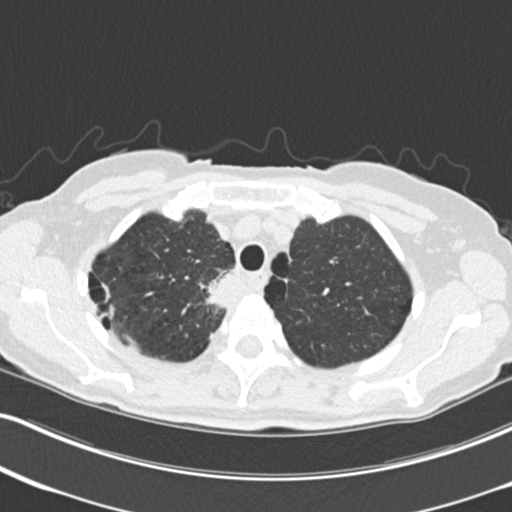
Axial slice from a low-dose chest CT screening exam; third annual screen; lung window (W 1500 / L -600 HU); 120 kVp; slice 45 of 226 in the series; 512 × 512 image matrix. Female participant, aged 68 years at enrolment. Current smoker at enrolment.
Expert reader's lesion annotation, bounding box <200,263,251,318> (left, top, right, bottom; pixels). Reader record for this screening exam (exam-level; its link to the box is not recorded): non-calcified nodule or mass ≥4 mm, right upper lobe, 31 × 29 mm, poorly defined margins, soft tissue attenuation, pre-existing on the prior screen: no. Official screen result: positive, other. Lung cancer was diagnosed 79 days after this screen: squamous cell carcinoma, NOS, right upper lobe, mediastinum, poorly differentiated (G3), stage IIIB (AJCC 6th edition), 43 mm at pathology.